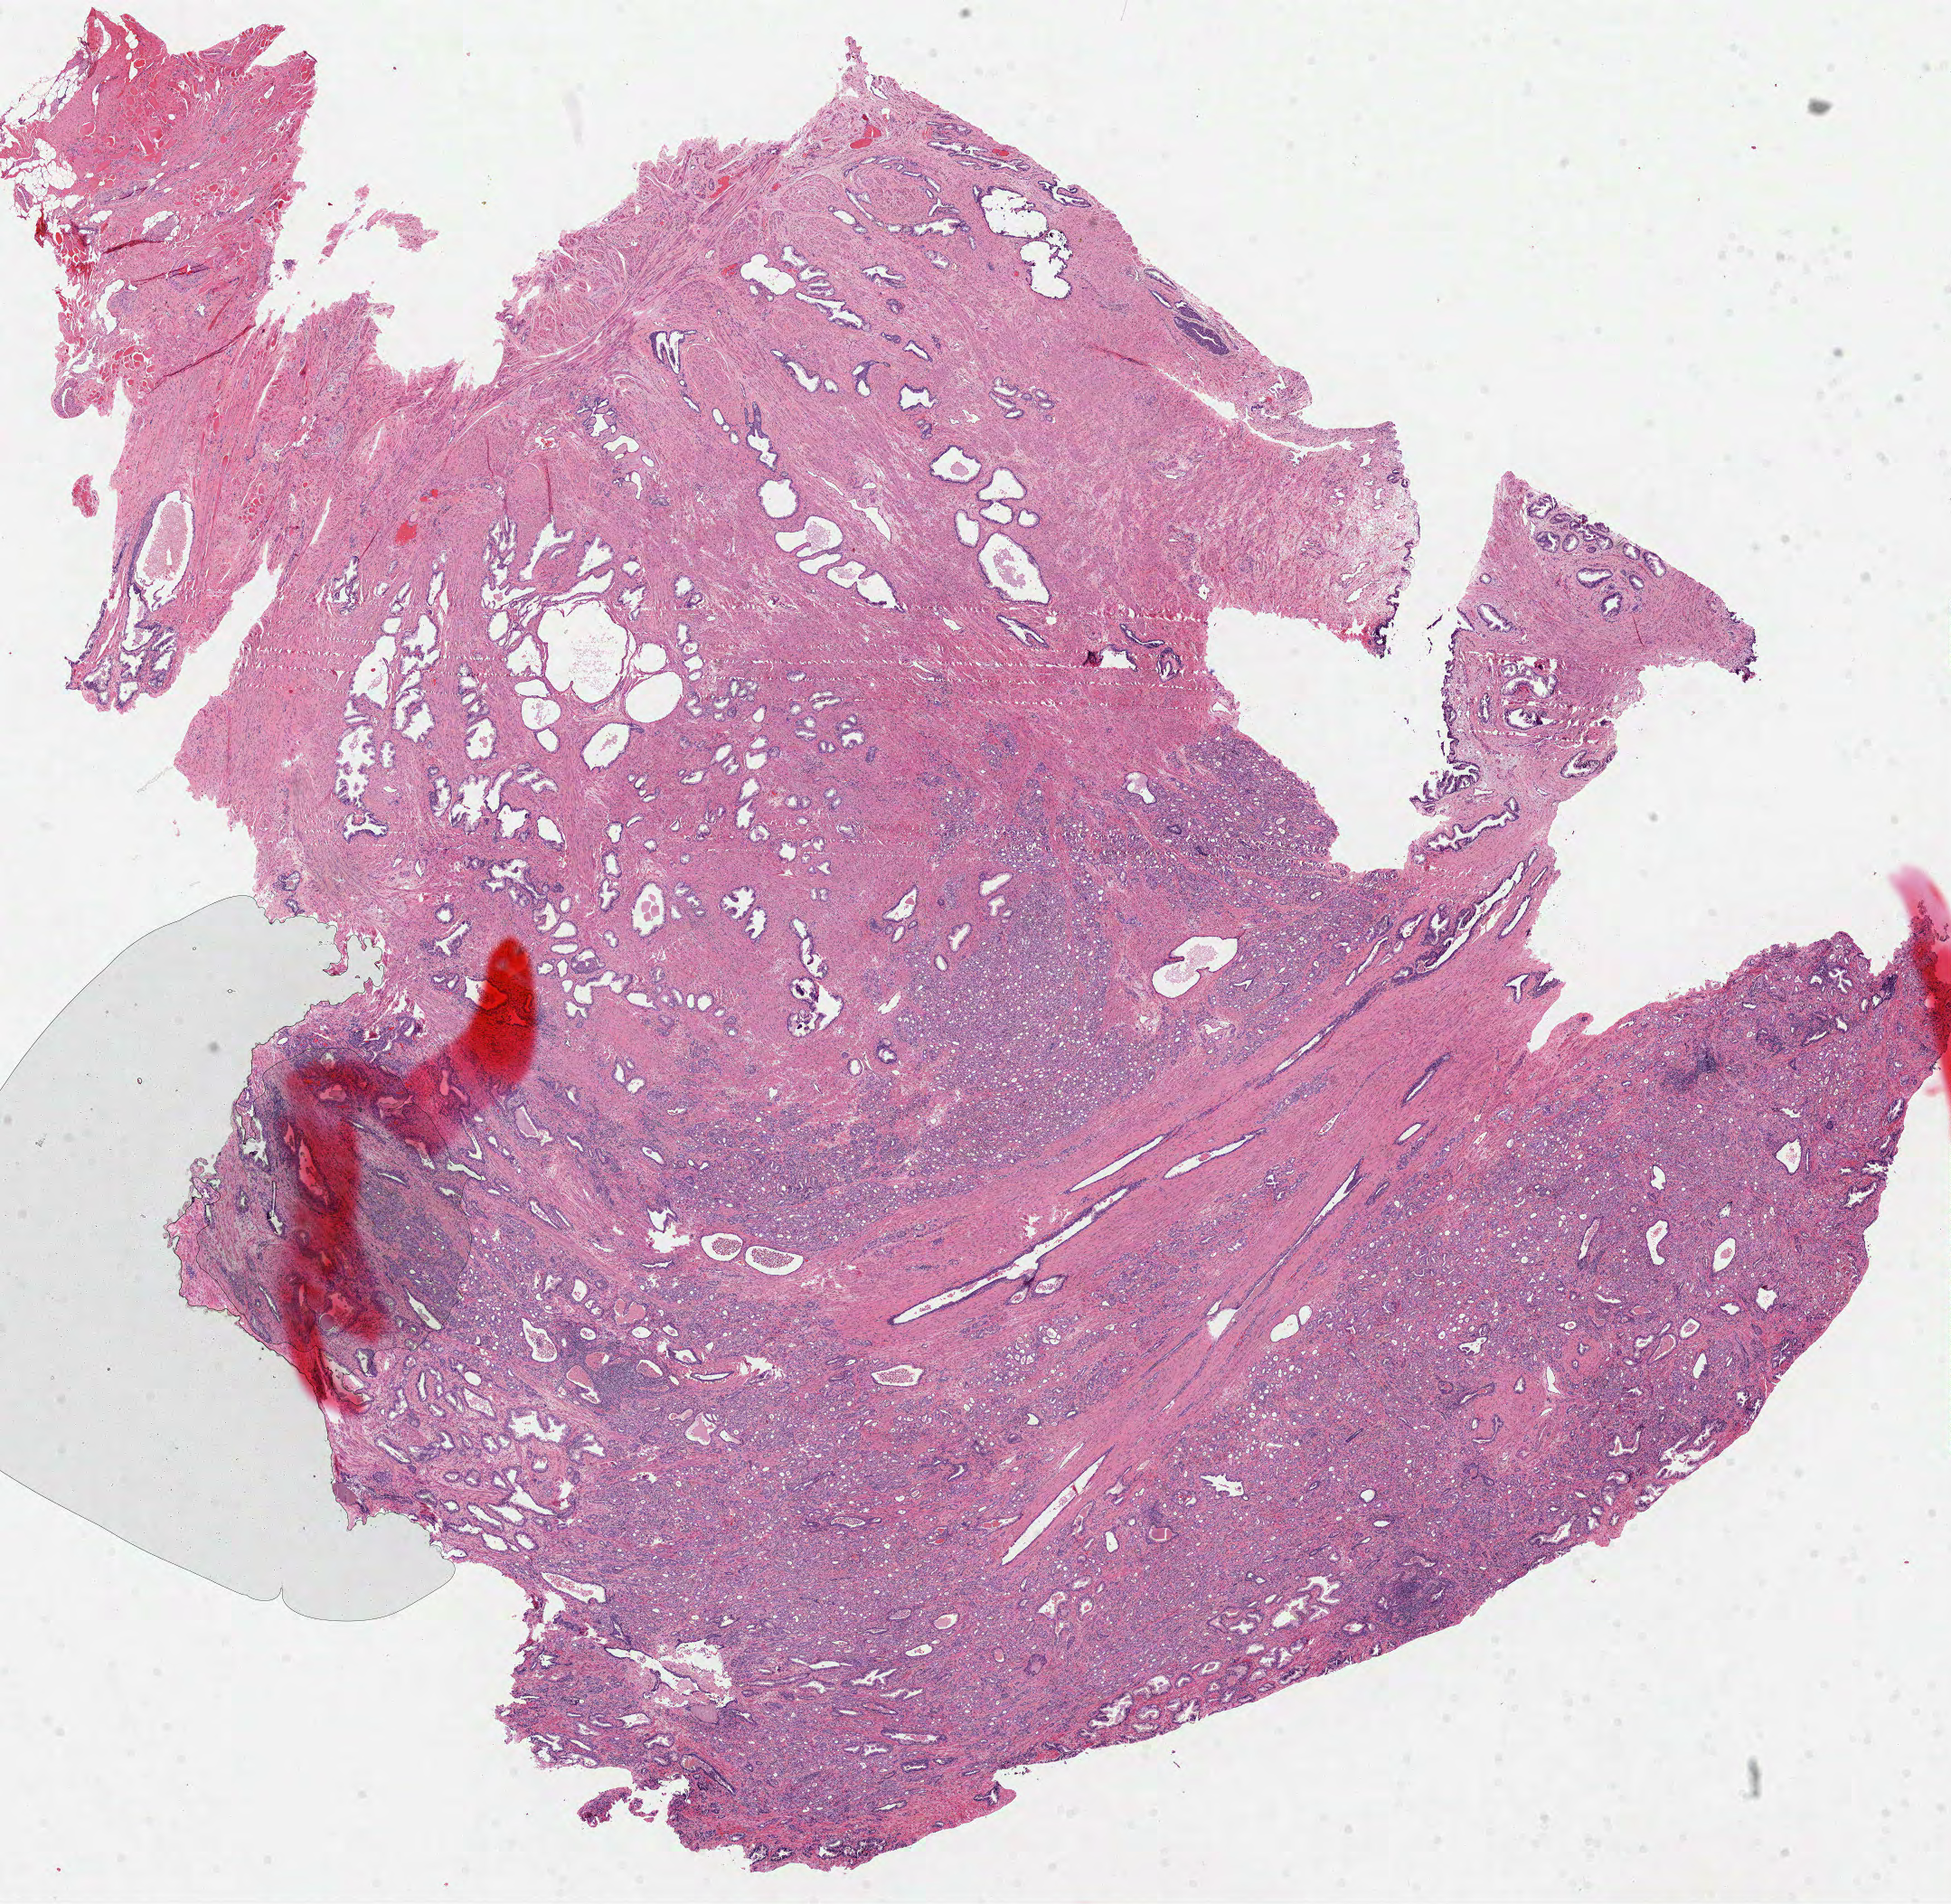
Digitized Hematoxylin and eosin (H&E) stained tissue section (whole slide), shown as a low-resolution overview of the whole scanned area (about 17.4 x 17.0 mm, from a 40x scan), FFPE section, primary tumour sample from the prostate. Male, age 55 years at initial diagnosis.
Histologic diagnosis: Acinar cell carcinoma (prostate gland).